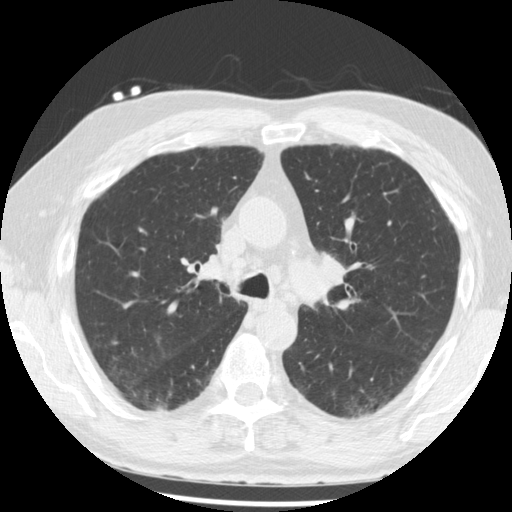
Low-dose screening chest CT, one axial slice; position 140 of 221 along the scan axis; 120 kVp; lung window (W 1500 / L -600 HU); 512 × 512 image matrix, field of view 350 × 350 mm.
Outlined on this slice (expert manual segmentation):
- lesion 1 (tumor, lower lobe of right lung): bounding box <153,407,177,413> (left, top, right, bottom; pixels)